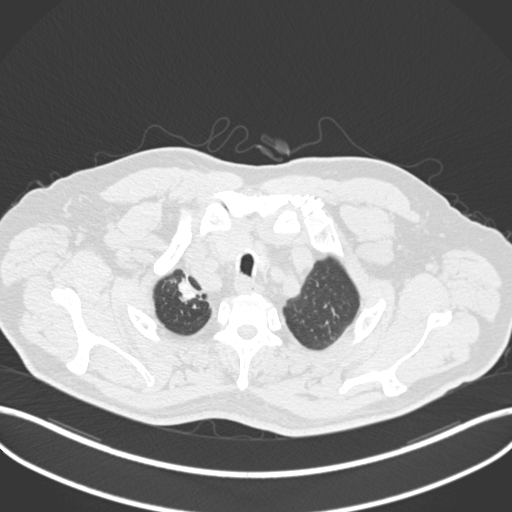
Chest CT, one axial slice; position 185 of 255 along the scan axis; reconstruction kernel B30f; lung window (W 1500 / L -600 HU); 1 mm slice thickness; 512 × 512 image matrix, field of view 400 × 400 mm. Male patient, age 60 years. From the clinical record (not read from this slice): clinical TNM (as recorded): T1b N1 M0.
Annotated regions visible in this slice (rectangle marked by the reading radiologist):
- lung tumour (recorded histology: squamous cell carcinoma): bounding box <169,275,205,311> (left, top, right, bottom; pixels)